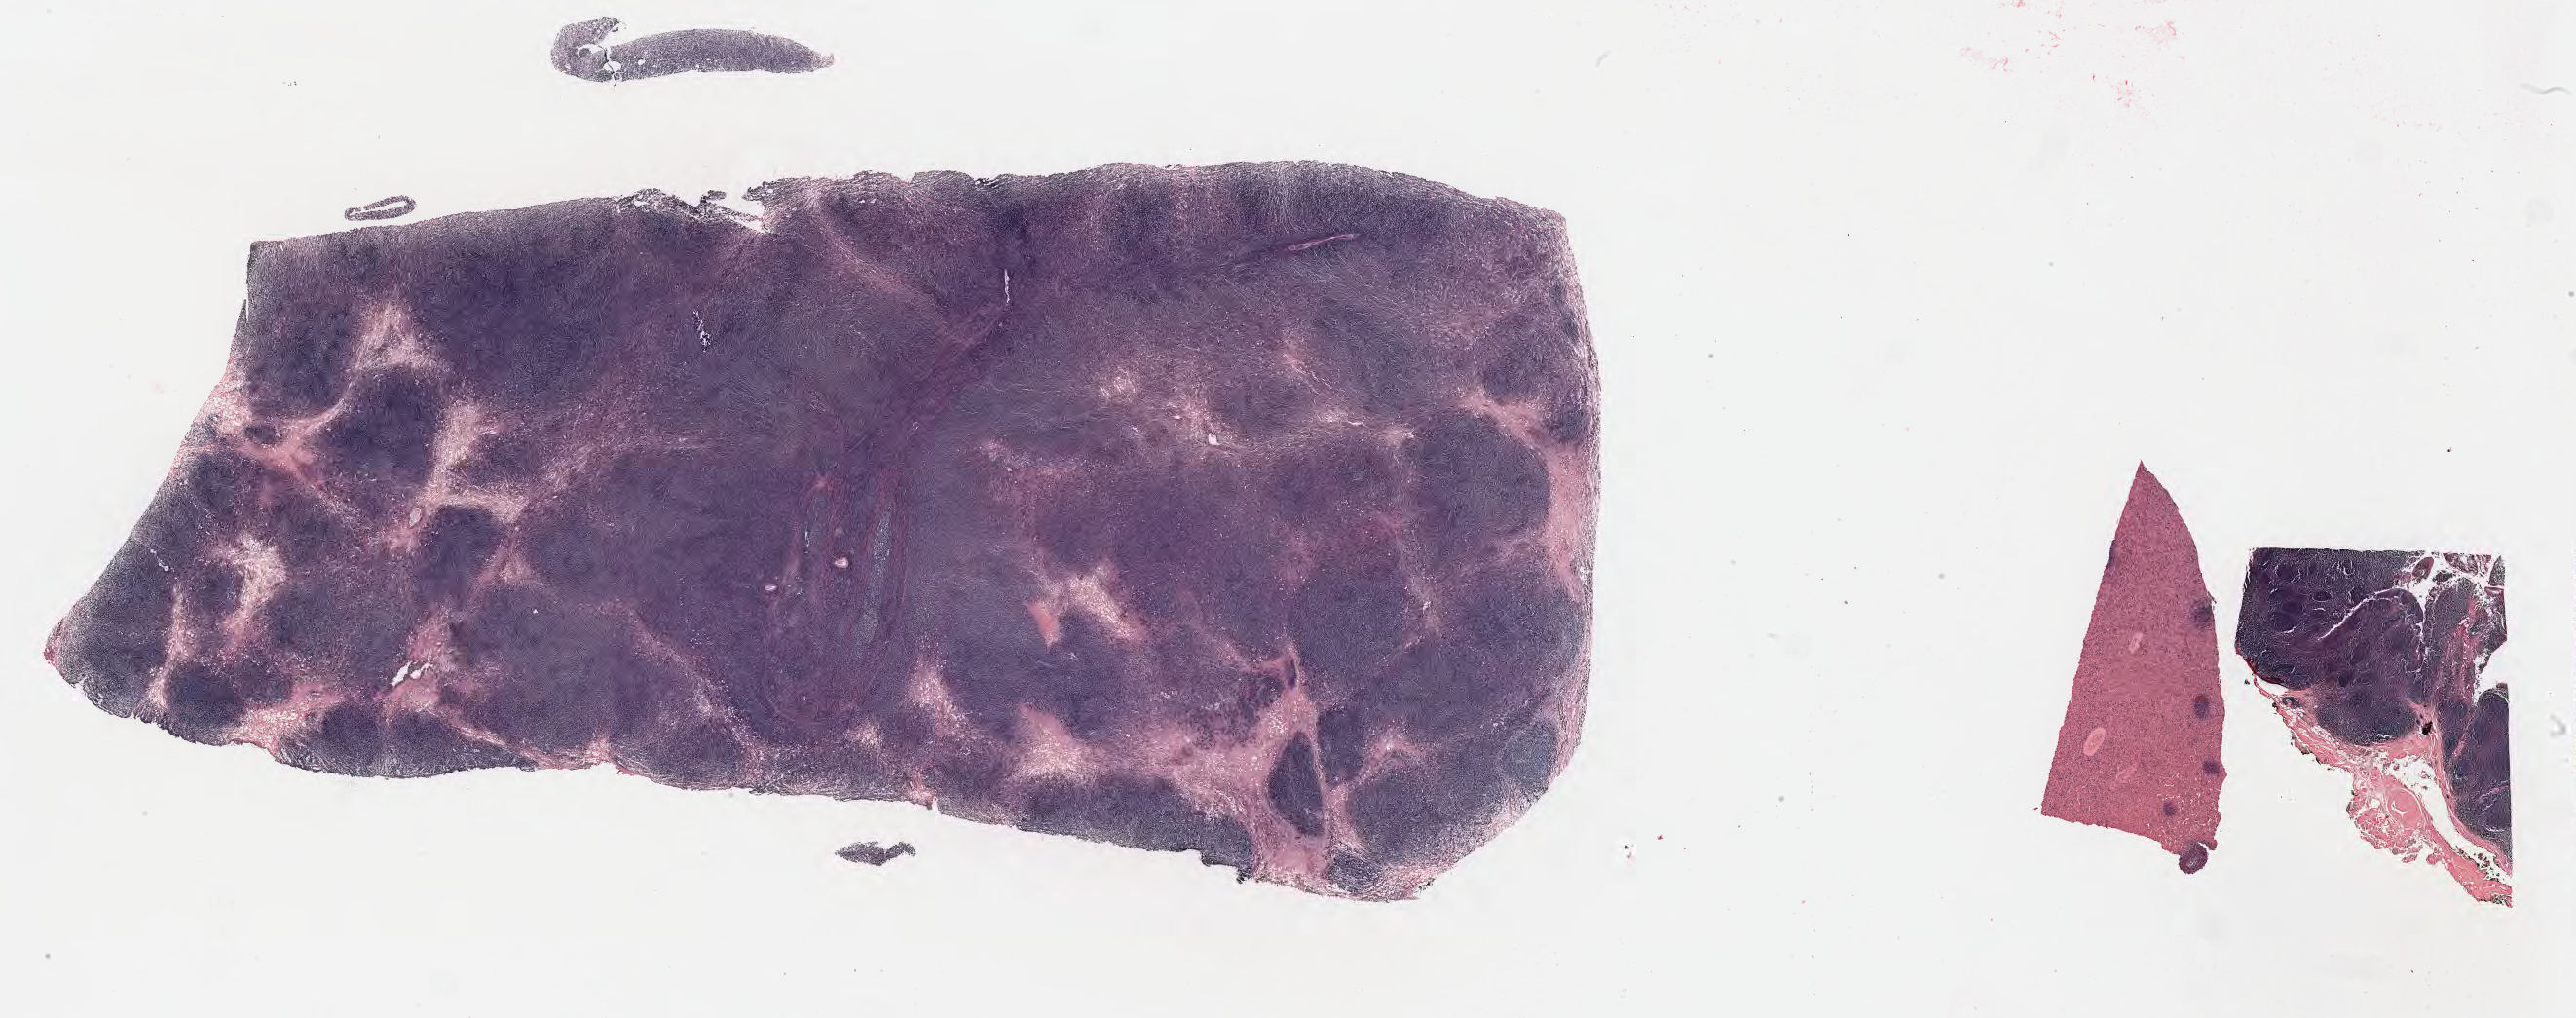
Whole-slide image; stain recorded as Iodonitrotetrazolium, shown as a low-resolution overview of the whole scanned area (about 42.8 x 16.9 mm). Tumor tissue. Patient male; 39 years old.
Histologic diagnosis: Diffuse large B-cell lymphoma, NOS.